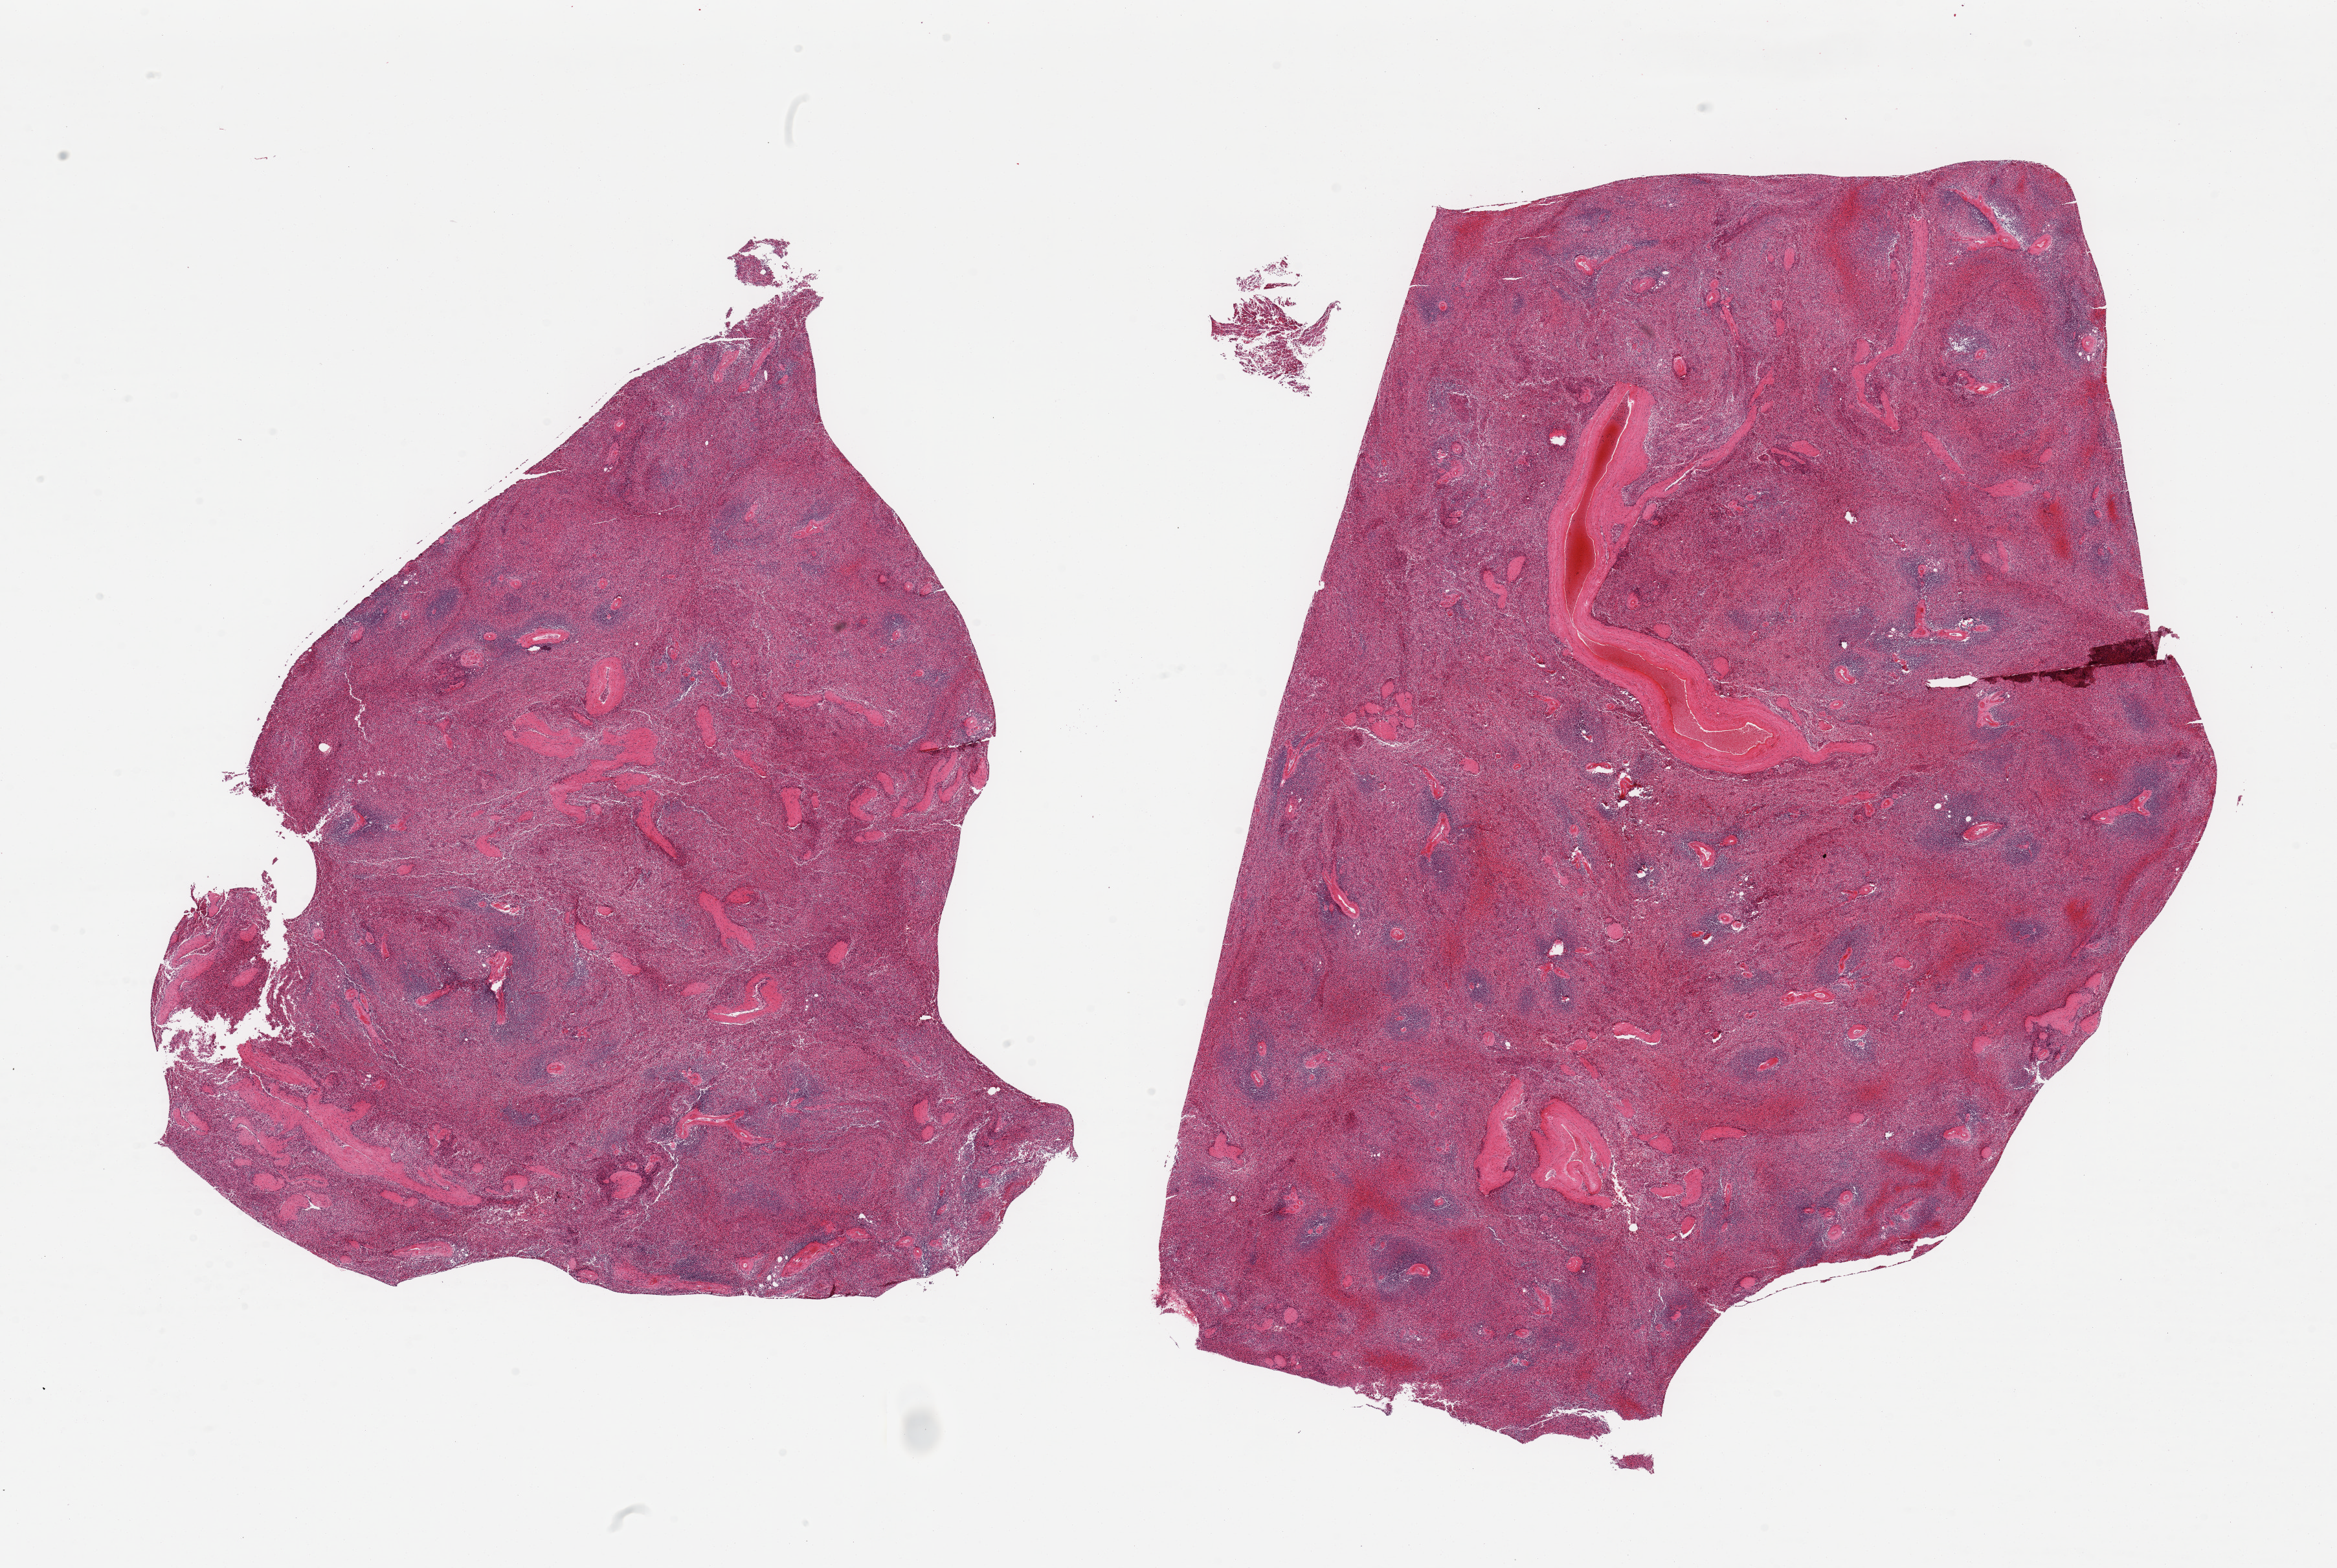
Haematoxylin and eosin whole-slide image — low-resolution overview of the scanned area, about 28.5 x 19.2 mm (slide scanned at 20x); PAXgene-fixed paraffin-embedded (PFPE) section; section of spleen (target tissue); donor tissue sample. Donor: male.
Review note (as recorded): 2 pieces, moderate congestion.